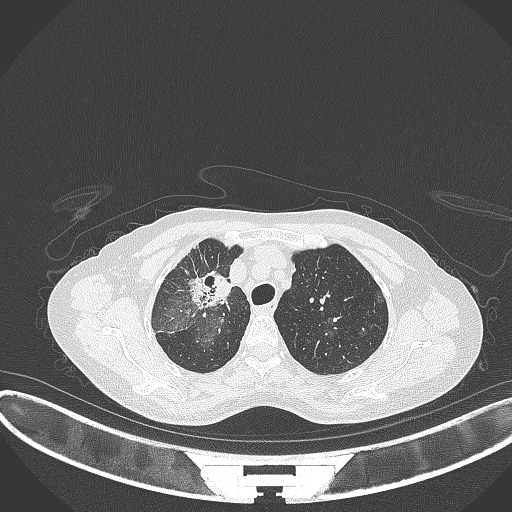
Chest CT, one axial slice. Slice 253 of 284 in the series (ordered by position). Reconstruction kernel B70f. Lung window (W 1500 / L -600 HU). 1 mm slice thickness. 512 × 512 image matrix, field of view 400 × 400 mm. Female patient, age 59 years. From the clinical record (not read from this slice): clinical TNM (as recorded): T3 N0 M0; histopathological grade: G1.
Structures marked on this image (rectangle marked by the reading radiologist):
- lung tumour (recorded histology: adenocarcinoma): bounding box (x1, y1, x2, y2) in pixels: (191, 268, 234, 313)